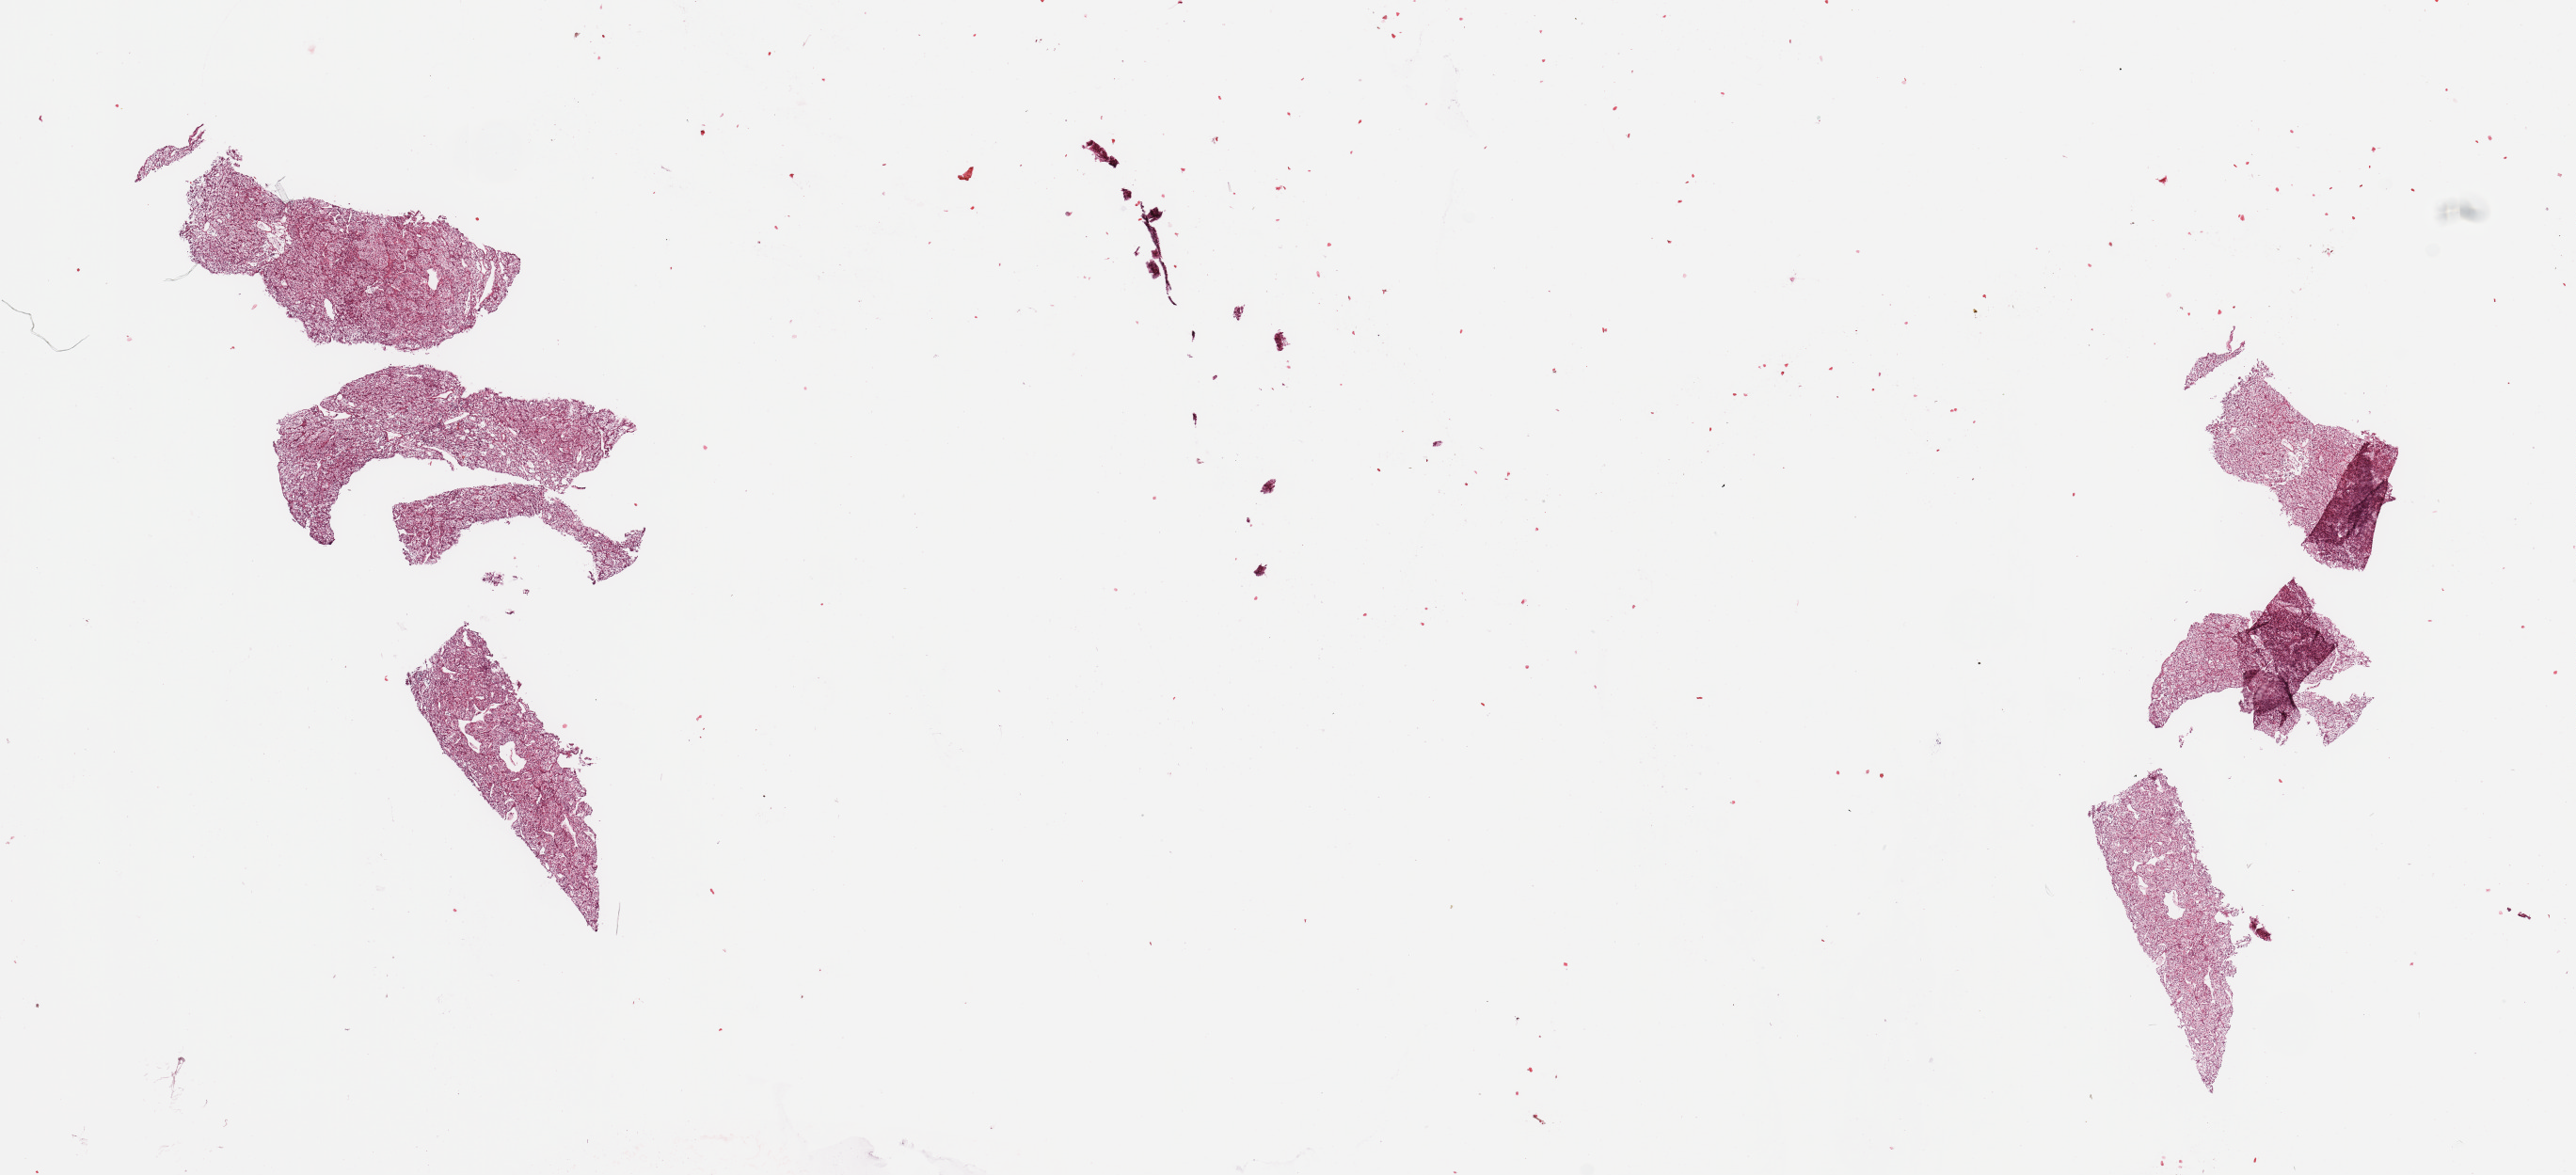
Digitized Hematoxylin and eosin (H&E) stained tissue section (whole slide), shown as a low-resolution overview of the whole scanned area (about 21.7 x 9.9 mm, from a 20x scan), kidney, tumour tissue. 58-year-old female patient. Histologic grade: G2 (moderately differentiated).
AJCC pathologic stage: III. Diagnosis: Renal cell carcinoma, NOS. Primary tumour site (as recorded): middle.